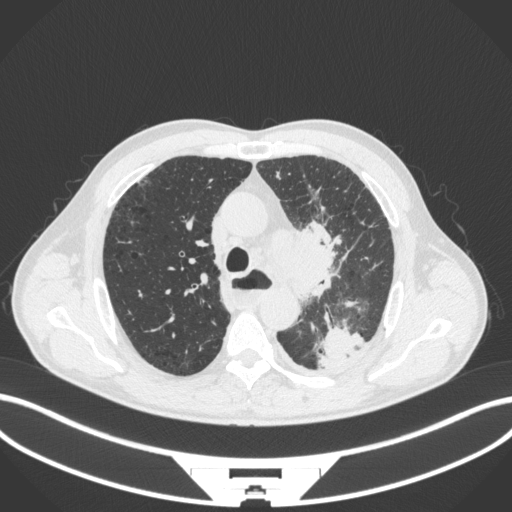
Chest CT, one axial slice; position 272 of 411 along the scan axis; reconstruction kernel B31f; 120 kVp; lung window (W 1500 / L -600 HU); 512 × 512 image matrix, field of view 400 × 400 mm. Male patient, age 57 years. From the clinical record (not read from this slice): clinical TNM (as recorded): T2a N1 M0.
Outlined on this slice (bounding box drawn by a radiologist):
- lung tumour (recorded histology: squamous cell carcinoma): bounding box (x1, y1, x2, y2) in pixels: (267, 223, 351, 302)